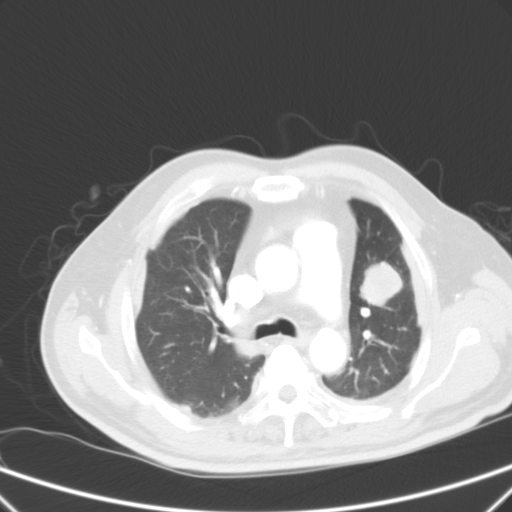
Chest CT, one axial slice. Position 40 of 59 along the scan axis. 120 kVp. Lung window (W 1500 / L -600 HU). 512 × 512 image matrix, field of view 357 × 357 mm. Patient: male, 66 years. From the clinical record (not read from this slice): clinical TNM (as recorded): T1c N3 M1a.
Annotated regions visible in this slice (bounding box drawn by a radiologist):
- lung tumour (recorded histology: squamous cell carcinoma): bounding box [x1, y1, x2, y2] px = [357, 257, 408, 309]